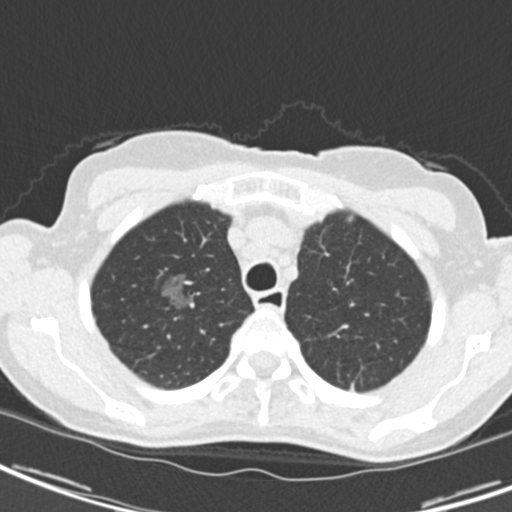
Low-dose screening chest CT, one axial slice. Slice 162 of 189 in the series (ordered by position). Reconstruction kernel B30f. 120 kVp. Lung window (W 1500 / L -600 HU). 2 mm slice thickness. 512 × 512 image matrix, field of view 279 × 279 mm.
Outlined on this slice (manually delineated by an expert):
- lesion 1 (tumor, upper lobe of right lung): bounding box (x1, y1, x2, y2) in pixels: (162, 274, 194, 308)